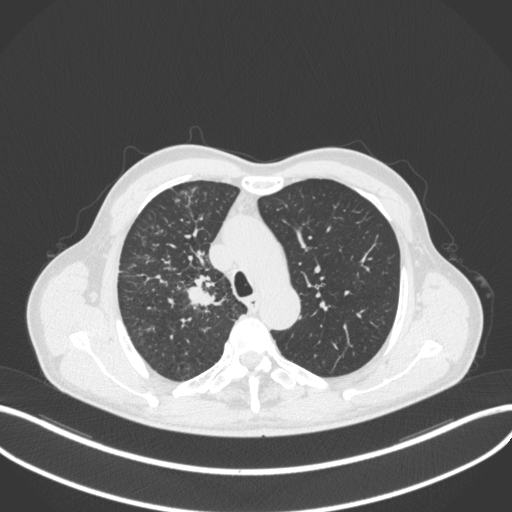
Chest CT, one axial slice; position 356 of 490 along the scan axis; reconstruction kernel B31f; lung window (W 1500 / L -600 HU); 512 × 512 image matrix, field of view 400 × 400 mm. Patient: male, 69 years. Case-level facts recorded for this patient, not image findings: clinical TNM (as recorded): T2a N0 M0.
Structures marked on this image (bounding box drawn by a radiologist):
- lung tumour (recorded histology: adenocarcinoma): bounding box (x1, y1, x2, y2) in pixels: (179, 271, 228, 310)